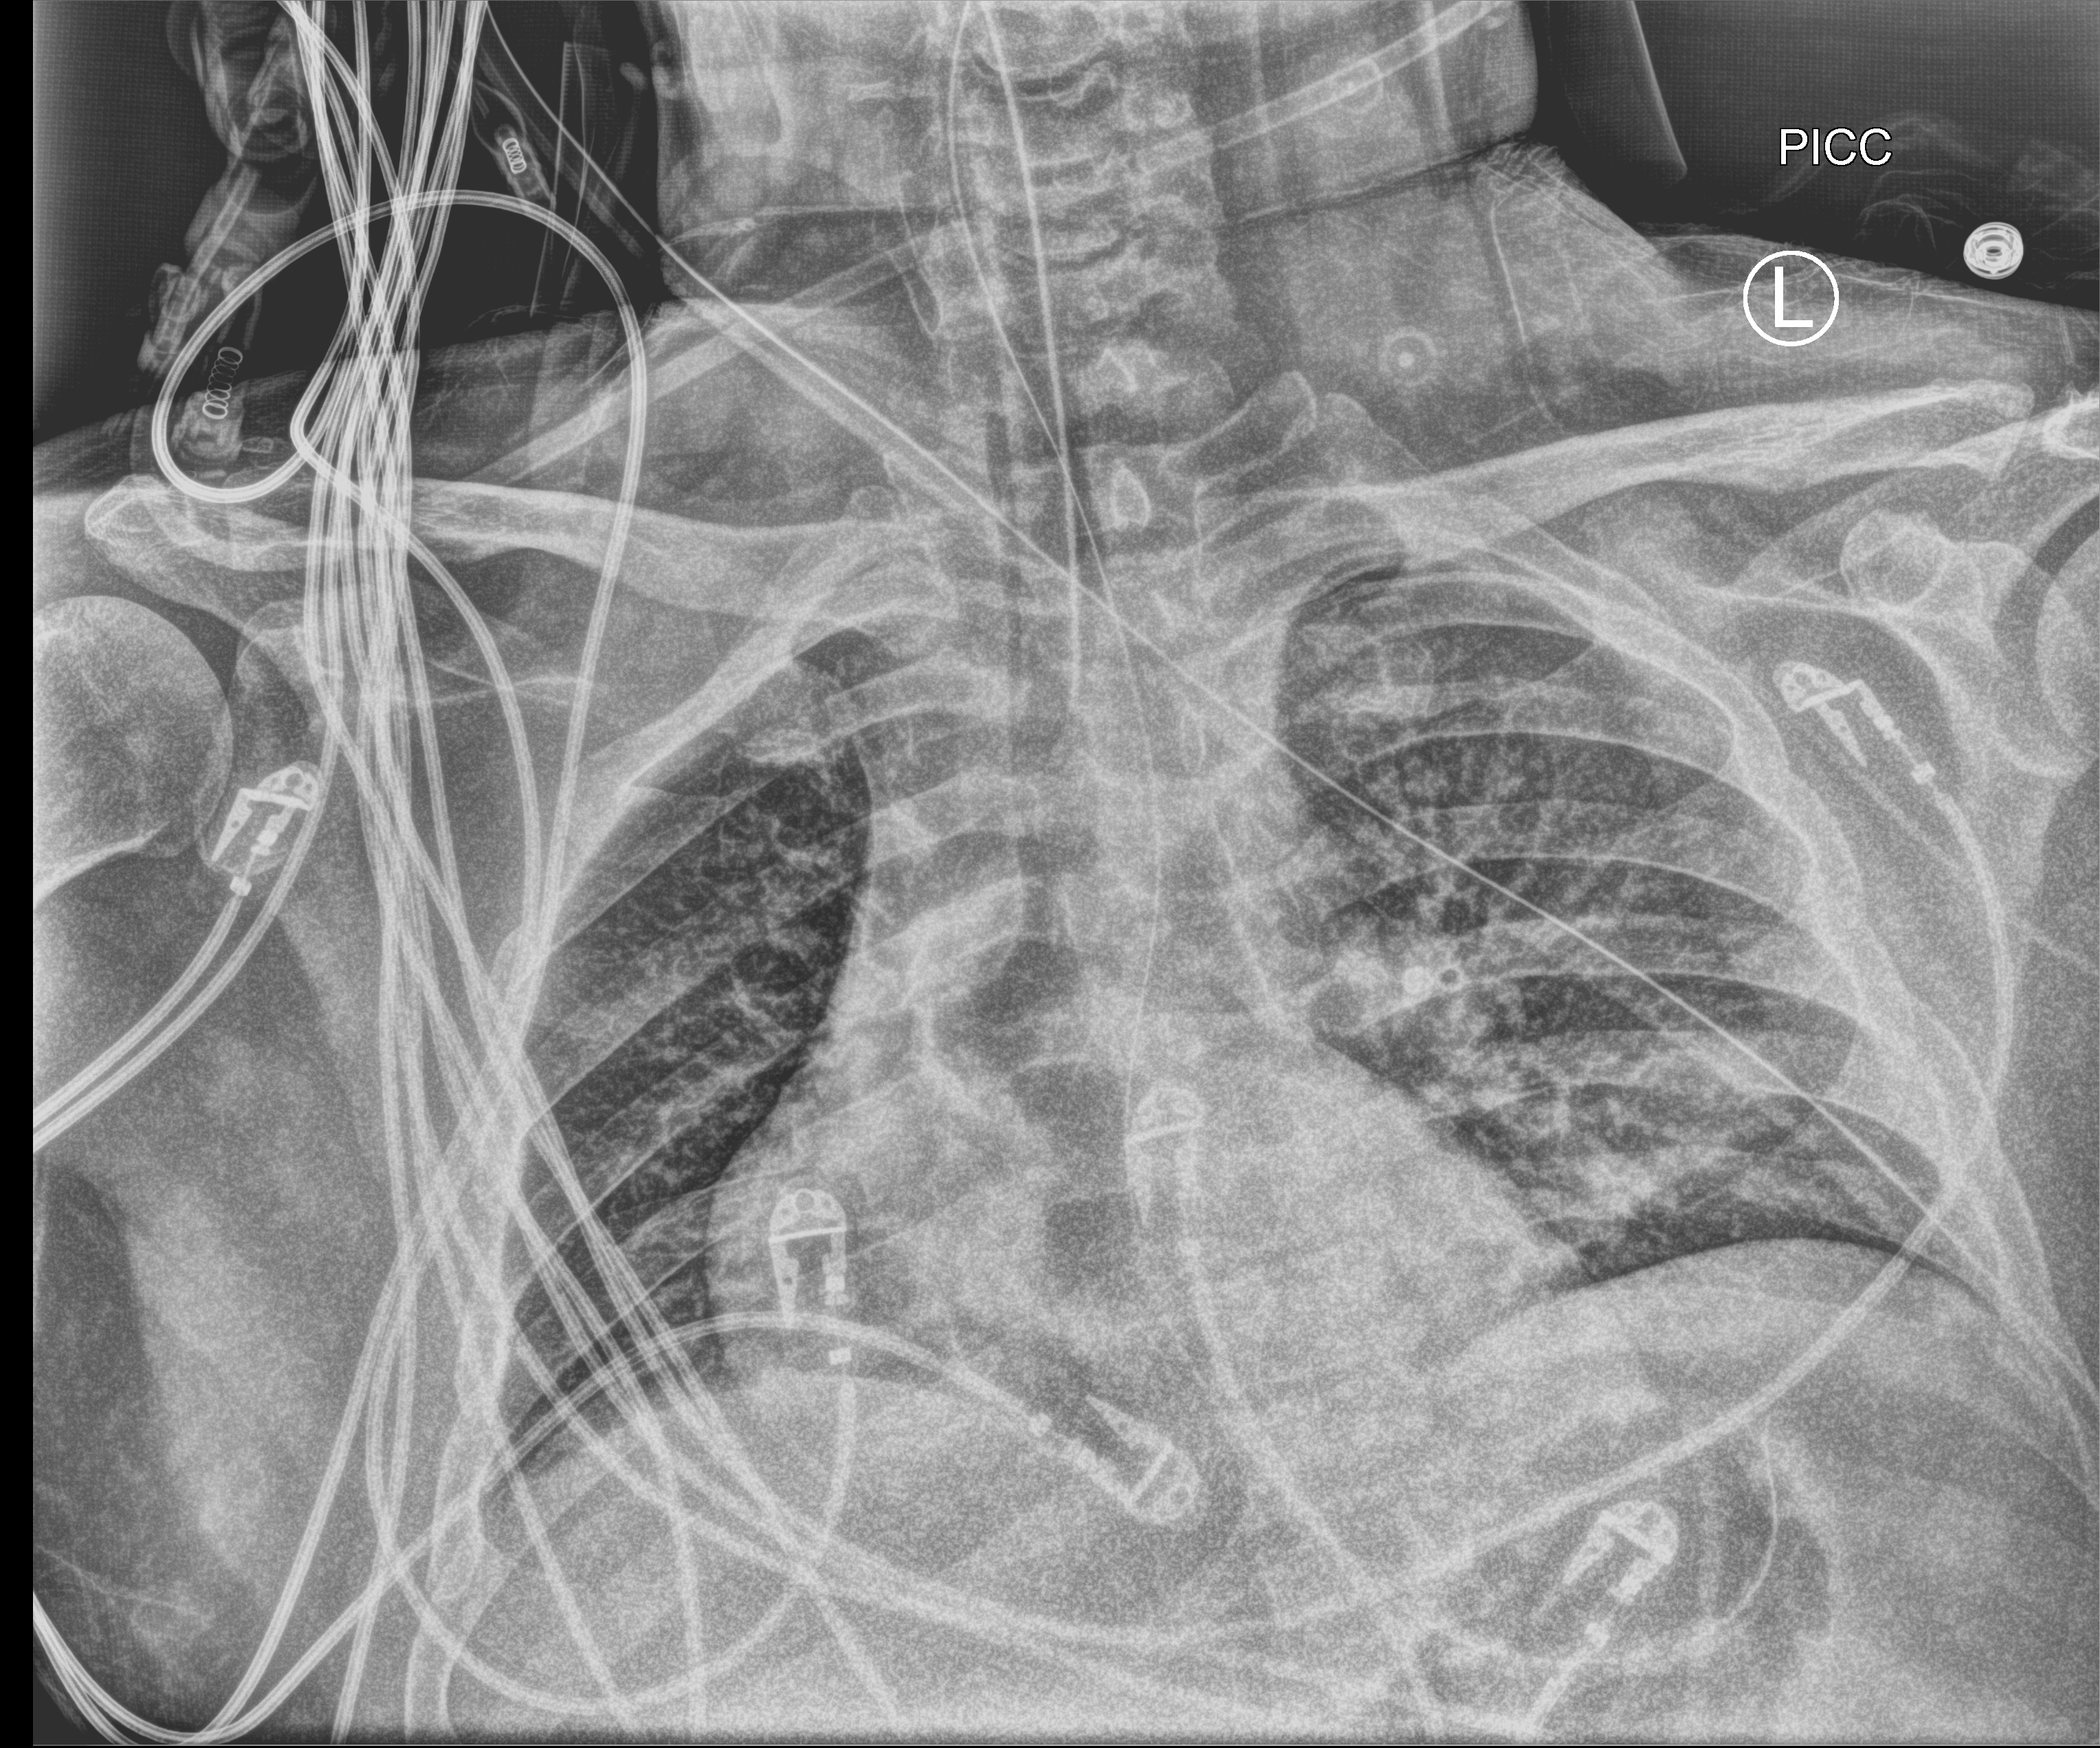
Portable chest radiograph. Patient hospitalised with COVID-19; male, aged 18–59 years.
Hospital-stay facts (about this admission, not read from this image; timing relative to this image not recorded): admitted to intensive care during this hospital stay: yes; length of hospital stay: 65 days; mechanically ventilated during this hospital stay: yes.